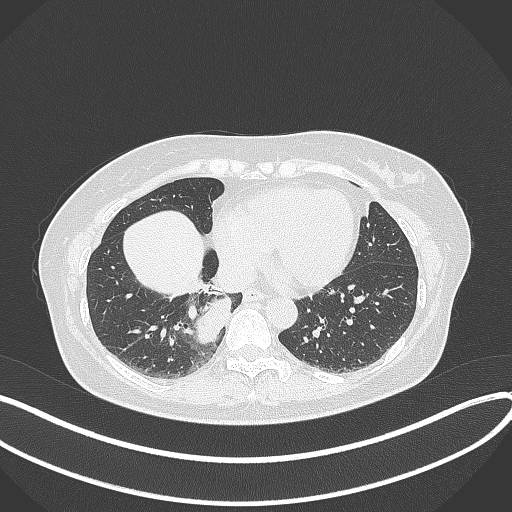
Chest CT, one axial slice; slice 112 of 331 in the series (ordered by position); lung window (W 1500 / L -600 HU); 1 mm slice thickness; 512 × 512 image matrix, field of view 400 × 400 mm. Patient: female, 54 years. From the clinical record (not read from this slice): clinical TNM (as recorded): T4 N0 M0.
Annotated regions visible in this slice (bounding box drawn by a radiologist):
- lung tumour (recorded histology: adenocarcinoma): box from (x=190, y=286) to (x=233, y=350) px